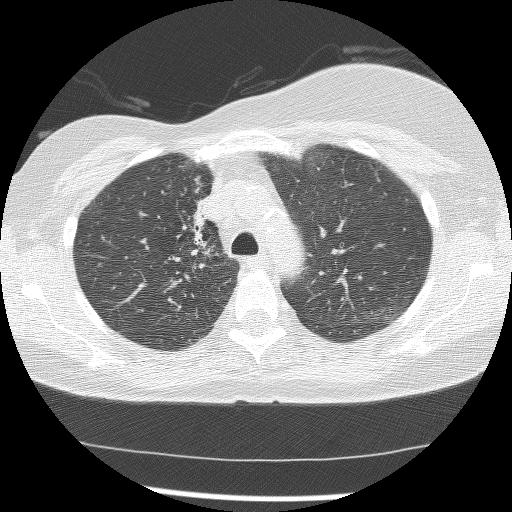
Chest CT (low-dose screening protocol), one axial image; baseline annual screen; lung window (W 1500 / L -600 HU); lung (sharp) reconstruction kernel (BONE); slice 41 of 172 in the series; 512 × 512 image matrix. Female participant, aged 56 years at enrolment.
Expert-annotated lung lesion, bounding box (x1, y1, x2, y2) in pixels: (164, 189, 222, 271). The screening reader recorded 2 non-calcified nodules or masses ≥4 mm on this exam; which of them this box marks is not recorded. Participant outcome: lung cancer diagnosed 1185 days after this screen (after the third annual screen) — adenocarcinoma, NOS, right upper lobe, stage IIIB (AJCC 6th edition), 8 mm at pathology.